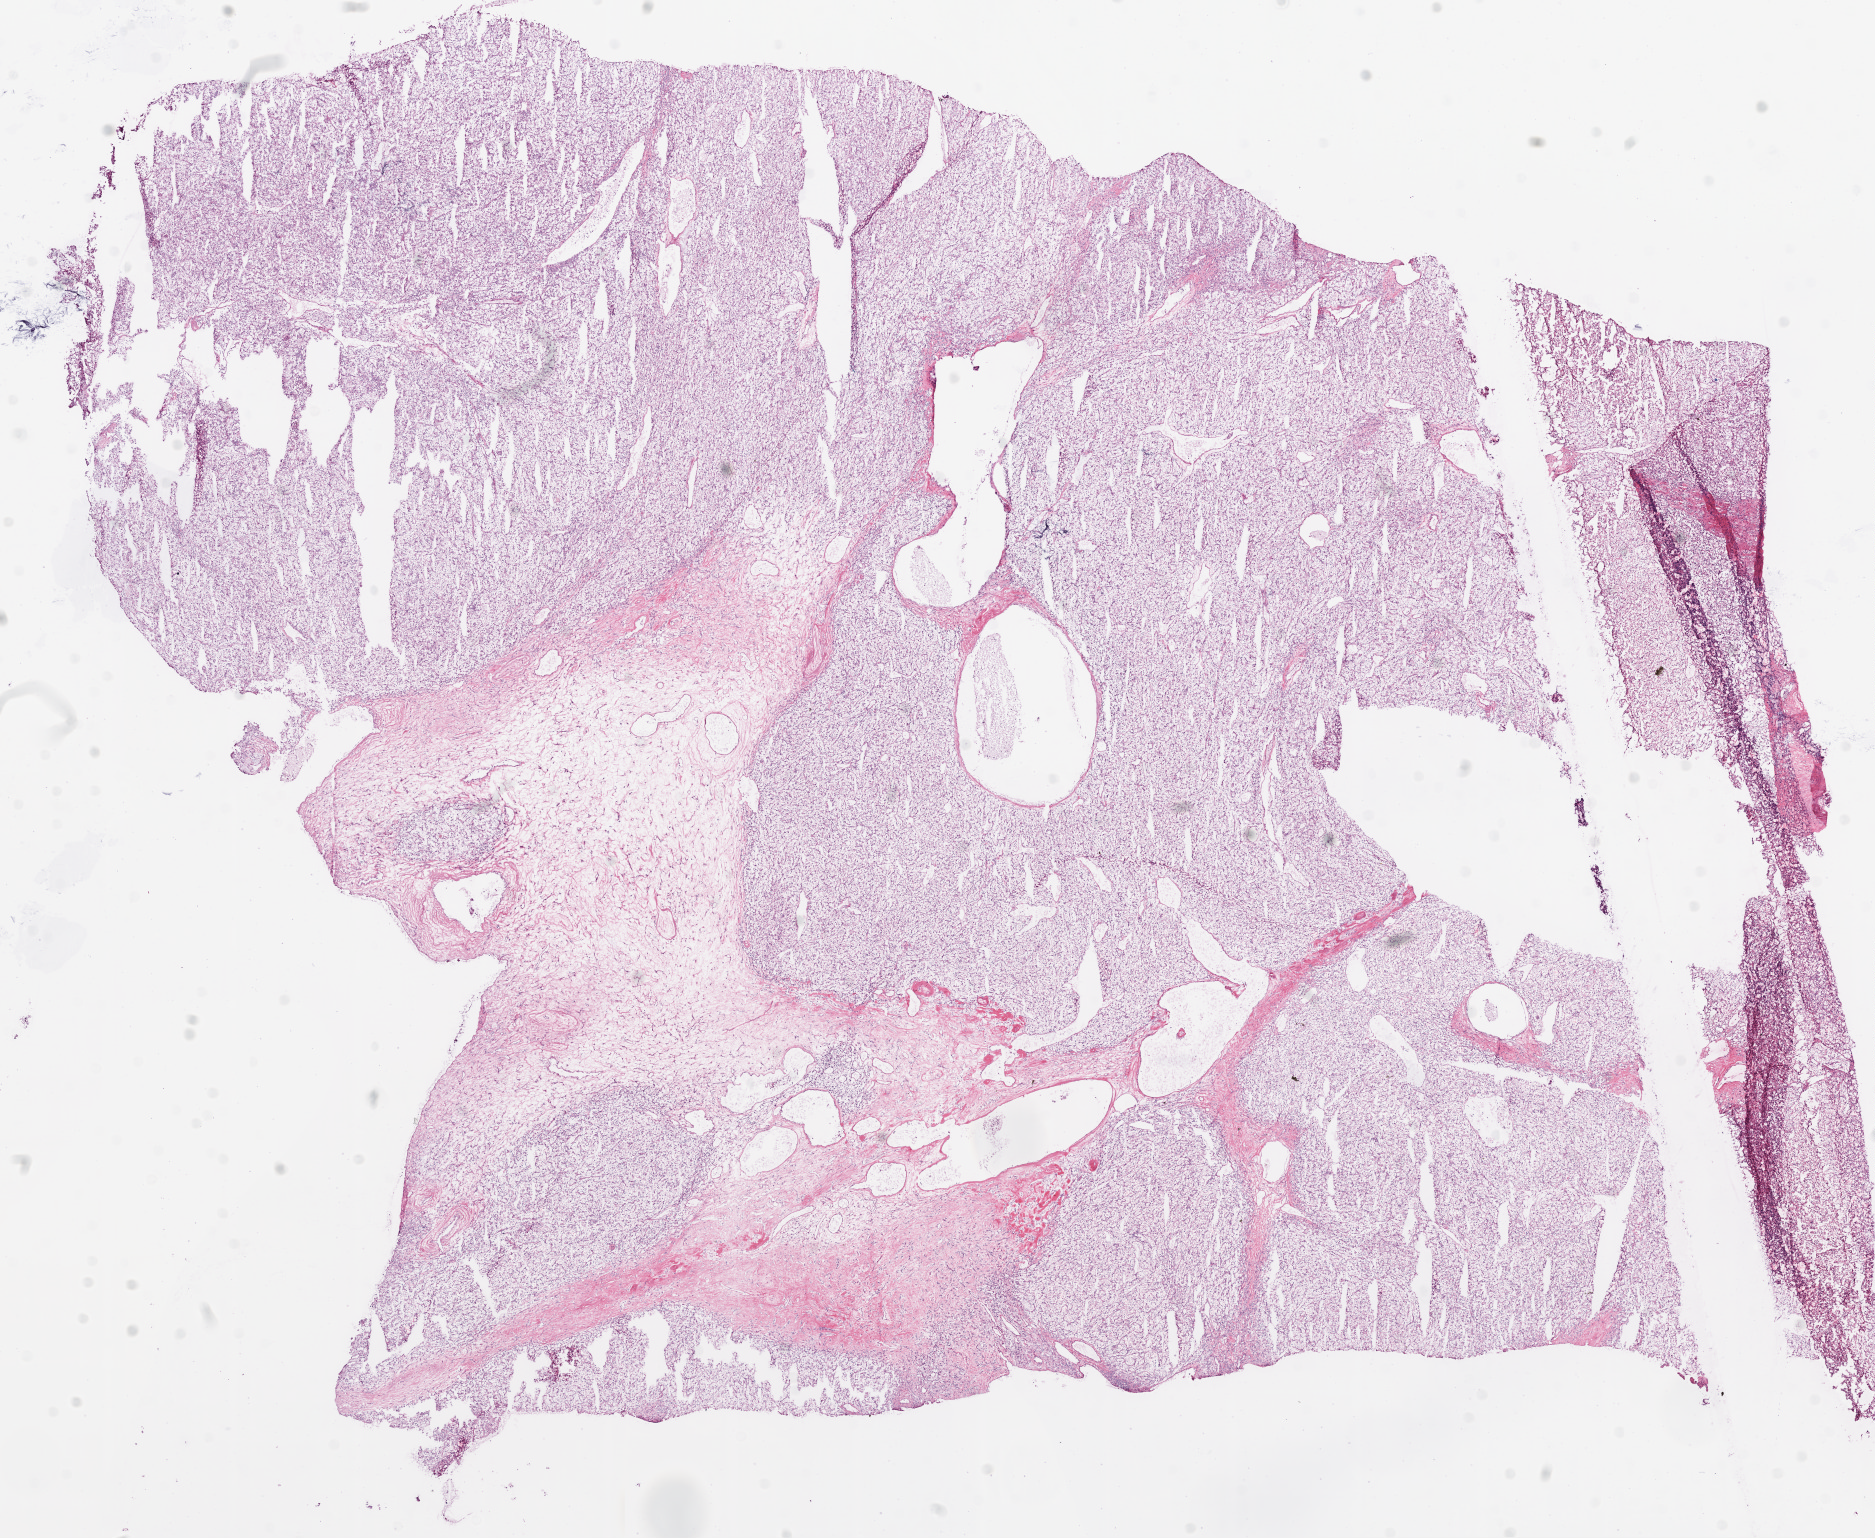
Whole-slide histology image, H&E-stained, whole scanned area (about 15.0 x 12.3 mm, acquisition: 20x scan) shown as a low-resolution overview, frozen section, primary tumour sample from the kidney. Patient: female, age at initial diagnosis 72 years. Histologic grade: G2 (moderately differentiated). Composition of this section per pathologist review: tumour cells 80%, tumour nuclei 90%, normal cells 0%, stromal cells 20%, necrosis 0%.
Lymph nodes positive (case pathology): 0 of 13 examined. Pathologic diagnosis: Clear cell adenocarcinoma, NOS. AJCC pathologic stage: I.